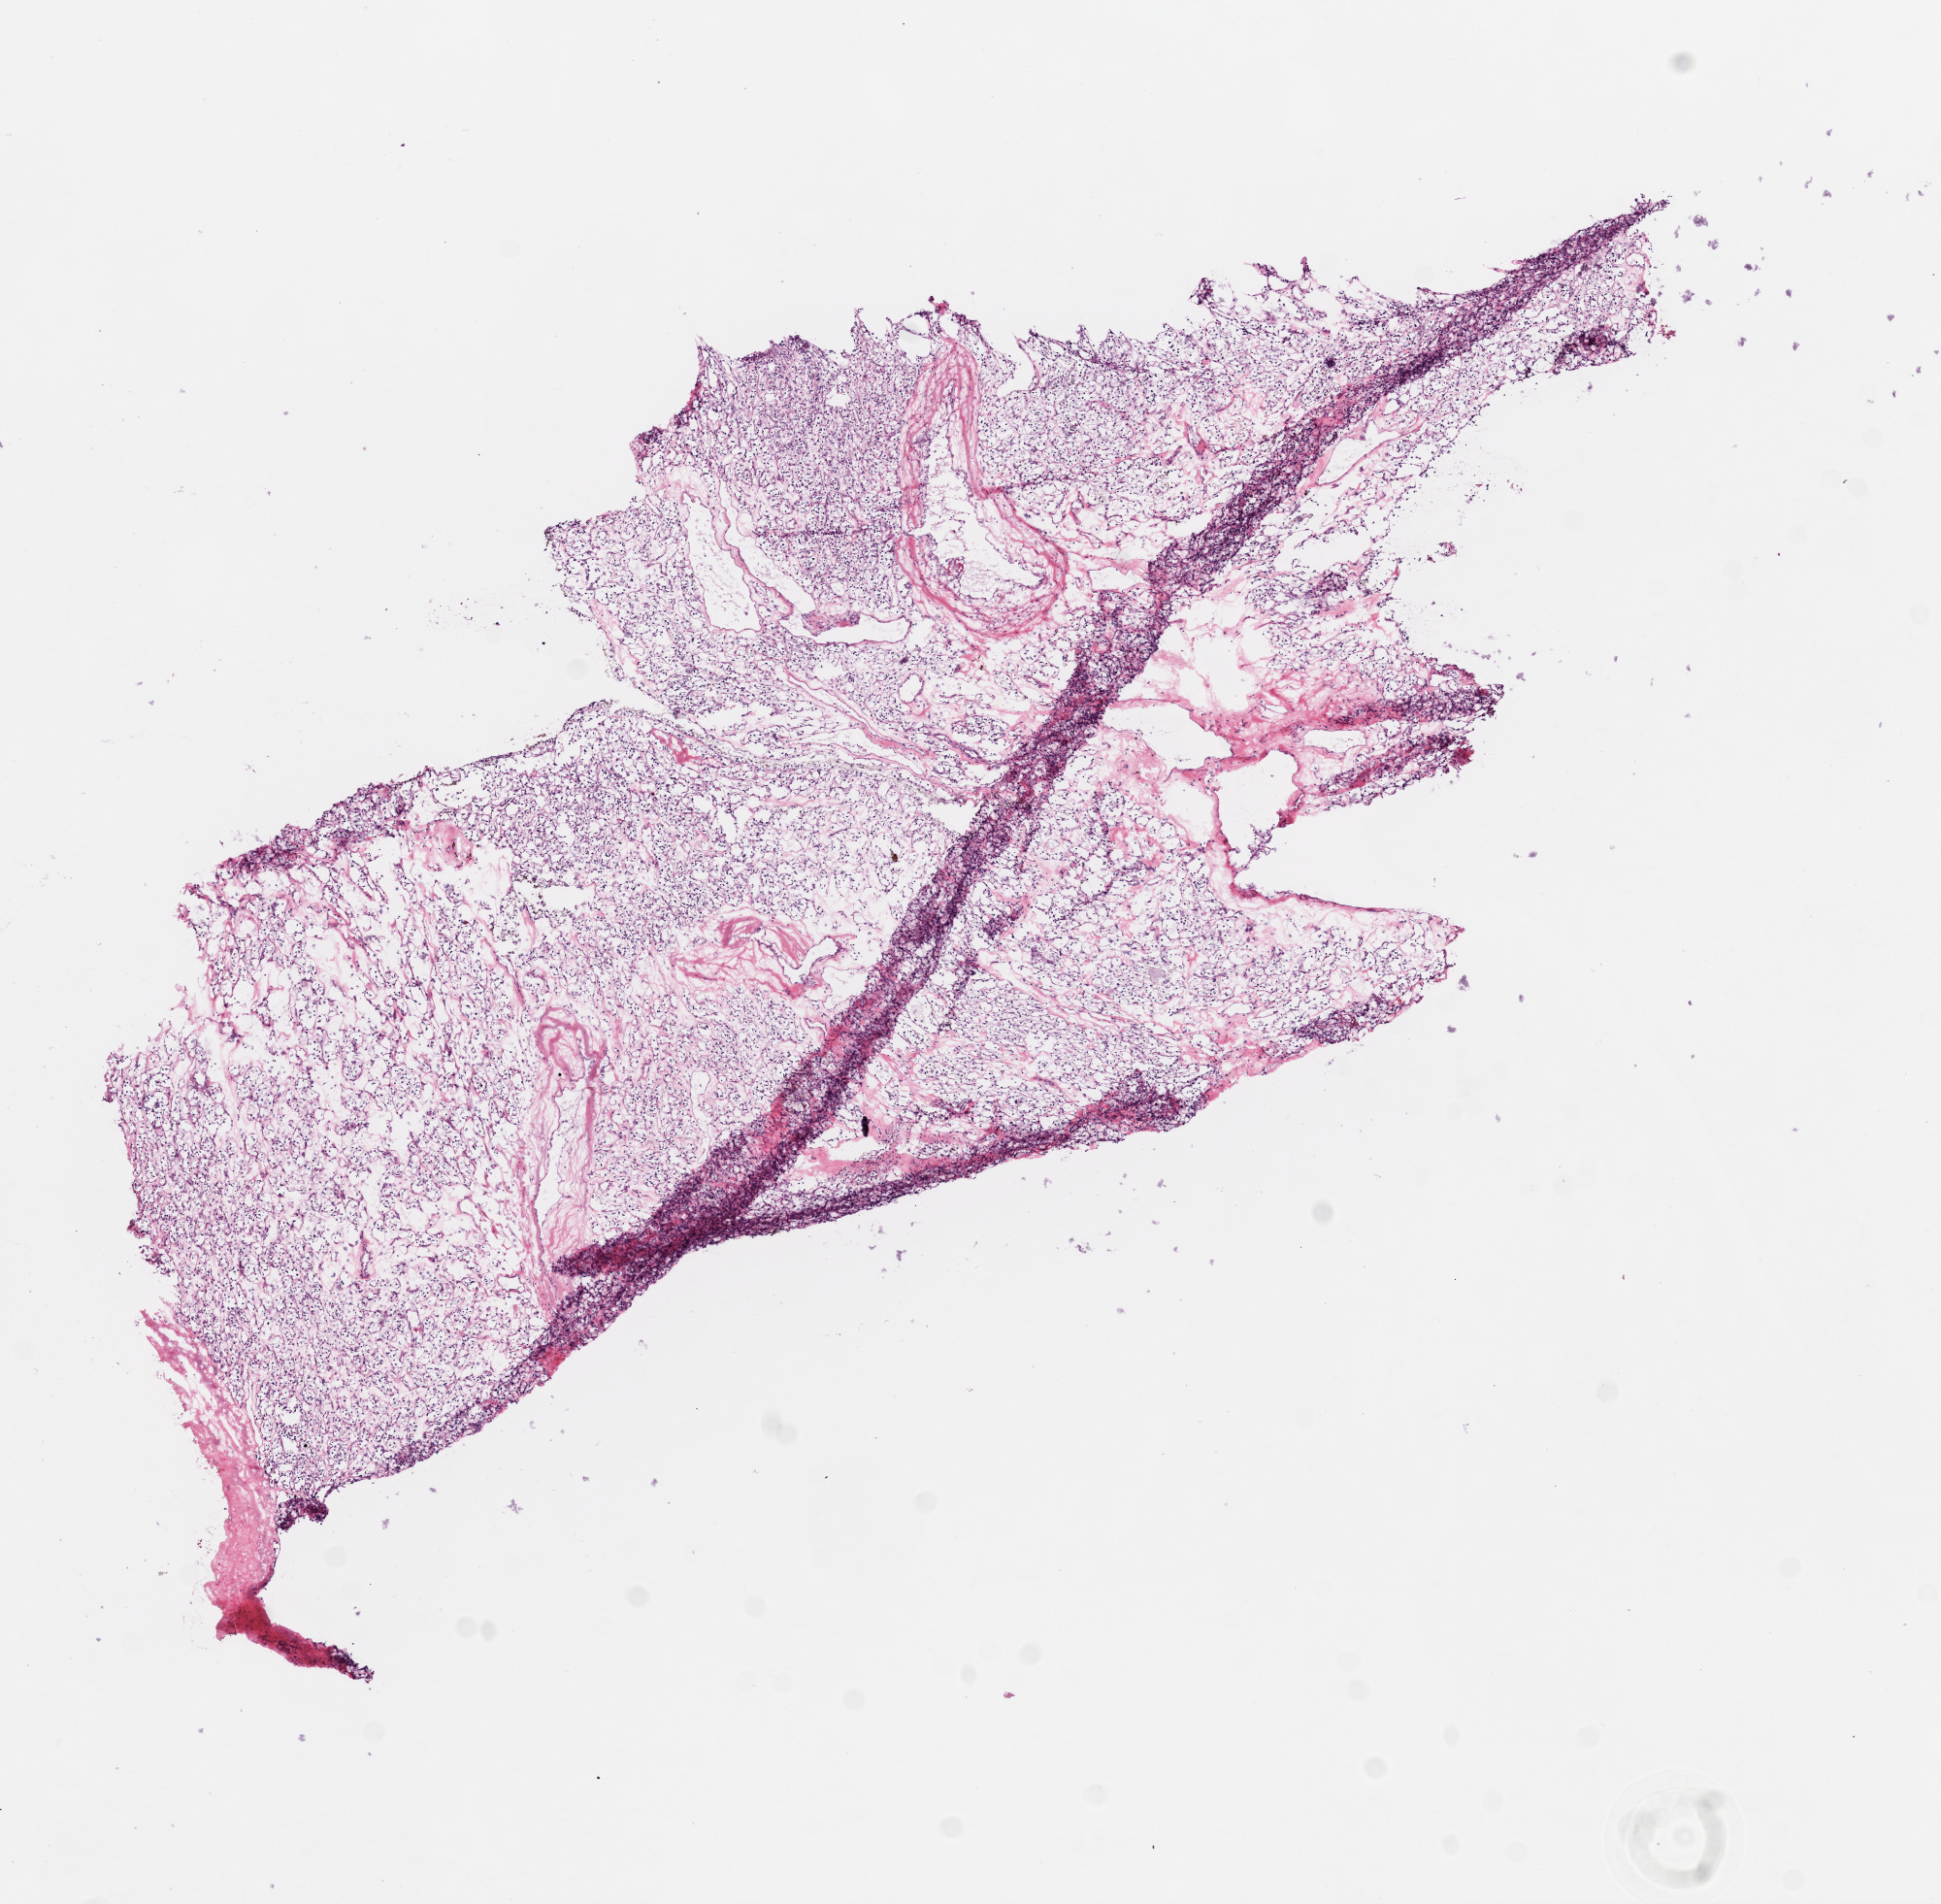
H&E-stained whole-slide image, whole scanned area (about 8.0 x 7.9 mm) shown as a low-resolution overview, frozen section from the top of the tissue portion, primary tumour sample from the kidney. Male, age 54 years at initial diagnosis. Histologic grade: G2 (moderately differentiated). Slide review estimates, as recorded: tumour cells 85%, tumour nuclei 80%, normal cells 0%, stromal cells 15%, necrosis 0%.
AJCC pathologic stage: I. Pathologic diagnosis: Clear cell adenocarcinoma, NOS.